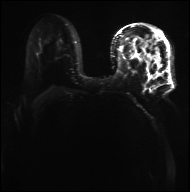
Breast MRI, one axial slice; position 17 of 36 along the scan axis; diffusion-weighted series; image 2 of 4 stored at this slice position (different b-values; order by instance number); 3 T; 4 mm slice thickness; 190 × 192 image matrix. Female patient.
Outlined on this slice (outlined manually by an expert reader):
- tumour on diffusion-weighted imaging: bounding box [x1, y1, x2, y2] px = [25, 39, 65, 68]